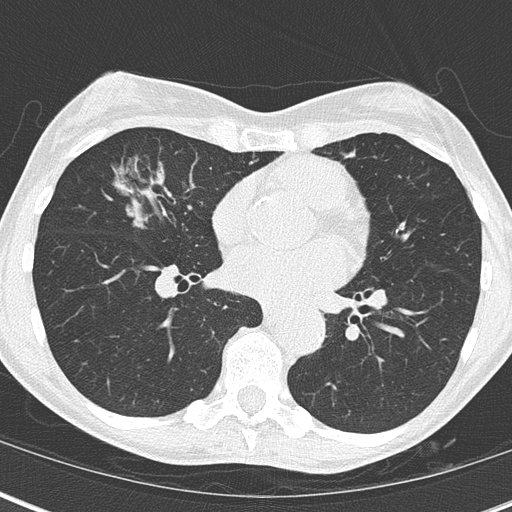
Low-dose screening chest CT, axial slice, third screening round (two years after baseline), lung window (W 1500 / L -600 HU), 512 × 512 image matrix. Female, age 67 years at enrolment. Current smoker at enrolment.
- Expert-annotated lung lesion, box from (x=96, y=149) to (x=200, y=251) px.
- Screening reader's record for this exam (one nodule recorded; not confirmed to be the boxed lesion): non-calcified nodule or mass ≥4 mm, right middle lobe, 32 × 17 mm, mixed attenuation, pre-existing on the prior screen: yes; interval growth: yes.
- Later outcome: lung cancer diagnosed 76 days after this screen — bronchiolo-alveolar adenocarcinoma, NOS, right middle lobe, well differentiated (G1), stage IA (AJCC 6th edition), 25 mm at pathology.